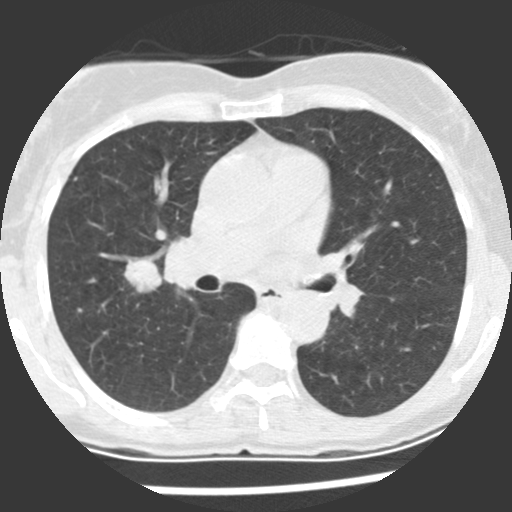
Low-dose screening chest CT, one axial slice; slice 124 of 225 in the series (ordered by position); 120 kVp; lung window (W 1500 / L -600 HU); 2.5 mm slice thickness; 512 × 512 image matrix, field of view 270 × 270 mm.
Structures marked on this image (manually delineated by an expert):
- lesion 1 (tumor, upper lobe of right lung): bounding box <124,259,161,293> (left, top, right, bottom; pixels)